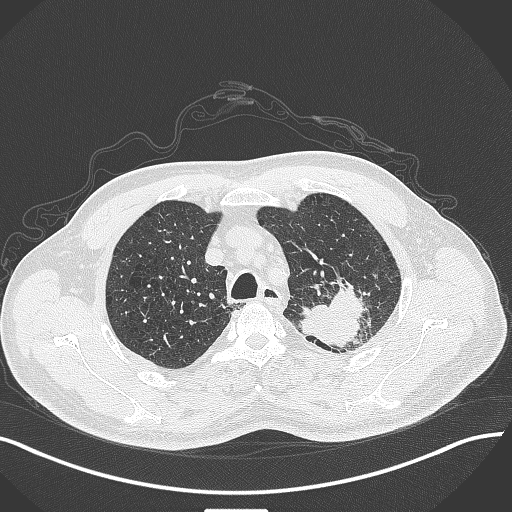
Chest CT, one axial slice; slice 336 of 429 in the series (ordered by position); 120 kVp; lung window (W 1500 / L -600 HU); 512 × 512 image matrix, field of view 400 × 400 mm. Patient: male, 55 years. From the clinical record (not read from this slice): clinical TNM (as recorded): T3 N0 M1c.
Annotated regions visible in this slice (rectangle marked by the reading radiologist):
- lung tumour (recorded histology: adenocarcinoma): bounding box [x1, y1, x2, y2] px = [292, 280, 373, 353]